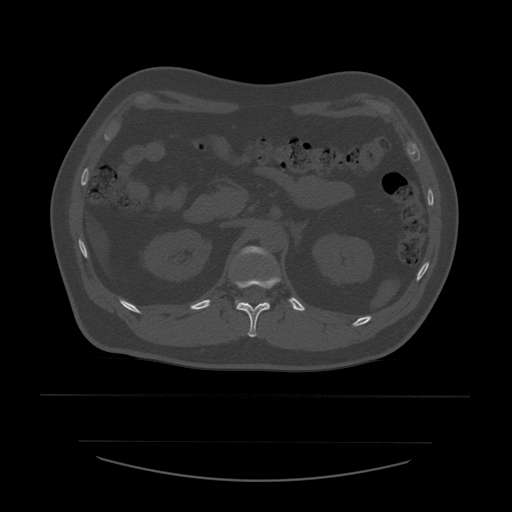
CT including the spine, one axial slice. 120 kVp. Bone window (W 1800 / L 400 HU). 512 × 512 image matrix, field of view 441 × 441 mm. Patient age 44 years. Case-level facts recorded for this patient, not image findings: primary cancer: soft tissue sarcoma.
Outlined on this slice (semi-automatically segmented with operator editing):
- L1 vertebra: box from (x=236, y=246) to (x=268, y=304) px
- T12 vertebra: (x=235, y=276)–(x=281, y=337)